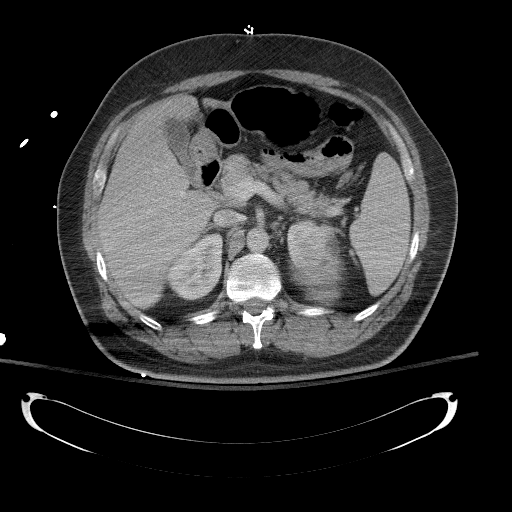
Contrast-enhanced abdominal CT, one axial slice. Position 86 of 154 along the scan axis. Reconstruction kernel B41f. 120 kVp. Soft-tissue window (W 400 / L 40 HU). 5 mm slice thickness. 512 × 512 image matrix, field of view 467 × 467 mm. Patient: male, 43 years. From the clinical record (not read from this slice): diagnosis: adrenocortical carcinoma; tumour side: left adrenal; tumour size at pathology: 9.8 cm; Ki-67 index: 30 %; stage (as recorded): 2.
Outlined on this slice (semi-automatic segmentation, software-assisted and operator-edited):
- mass: bounding box <292,241,342,303> (left, top, right, bottom; pixels)